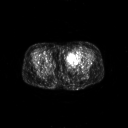
FDG PET of an extremity soft-tissue mass (from a PET/CT study), one axial slice. Position 21 of 267 along the scan axis. 3.27 mm slice thickness. 128 × 128 image matrix, field of view 700 × 700 mm. Female patient, age 47 years. From the clinical record (not read from this slice): histological type: myxofibrosarcoma; grade: intermediate; site of the primary tumour: left thigh.
Outlined on this slice (expert contour drawn on MRI and transferred to this co-registered scan by the dataset authors):
- gross tumour volume including surrounding oedema: box from (x=66, y=51) to (x=82, y=65) px
- gross tumour volume (mass): (x=66, y=52)–(x=81, y=64)